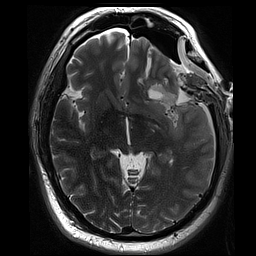
Brain MRI from a brain-tumour surgery series, one axial slice. Position 47 of 70 along the scan axis. 2 mm slice thickness. 256 × 256 image matrix, field of view 220 × 220 mm. From the clinical record (not read from this slice): histopathology: Oligodendroglioma; WHO grade: 3; IDH mutation: yes; tumour location: Left Sylvian Fissure (Temporal).
Structures marked on this image (expert manual segmentation):
- residual tumour: box from (x=152, y=84) to (x=177, y=107) px